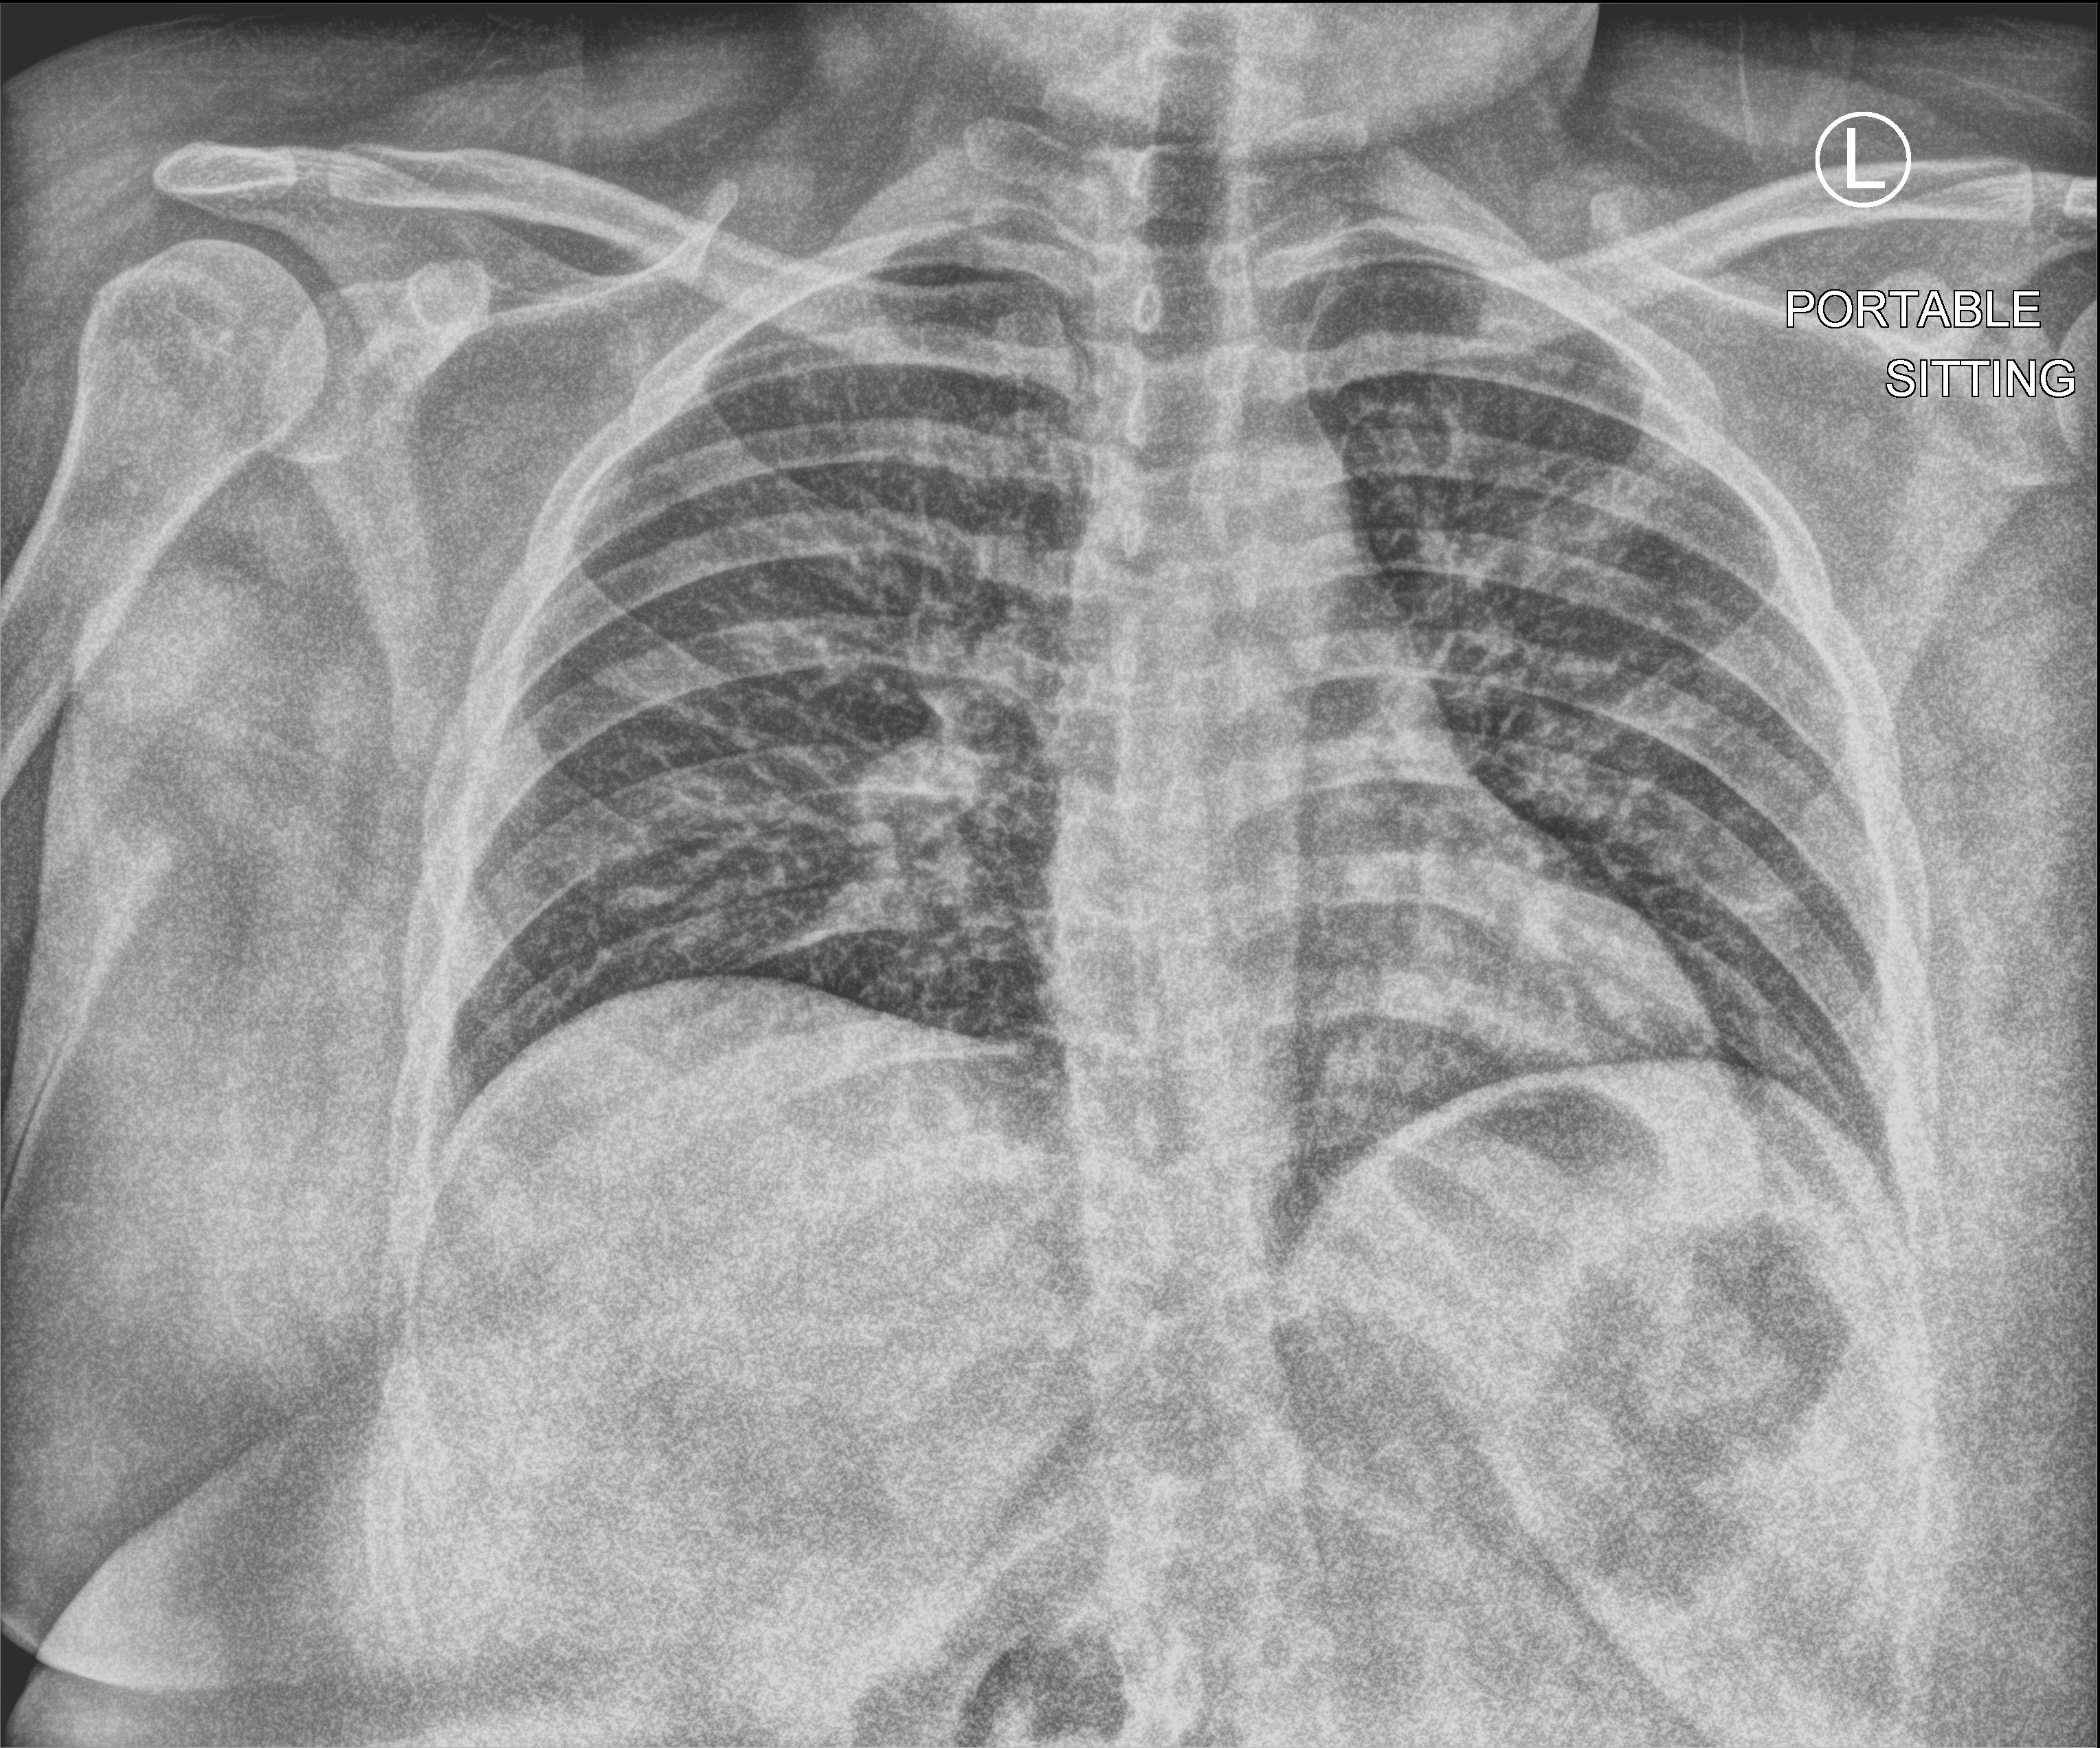
Portable chest radiograph; anteroposterior (AP) projection. Patient hospitalised with COVID-19; female, aged 18–59 years.
From the hospital-stay record, not from the radiograph (when in the stay this image was taken is not recorded): admitted to intensive care during this hospital stay: no; mechanically ventilated during this hospital stay: no.